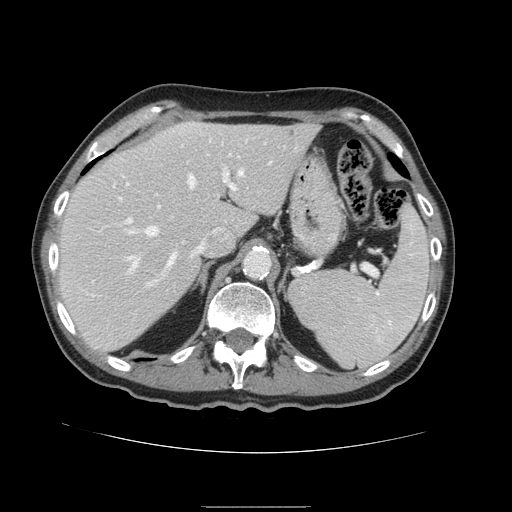
Contrast-enhanced abdominal CT, one axial slice; position 108 of 168 along the scan axis; soft-tissue window (W 400 / L 40 HU); 512 × 512 image matrix. Male patient, age 74 years. From the clinical record (not read from this slice): diagnosis: colorectal cancer liver metastases, imaged before liver resection; multiple liver metastases: no; largest metastasis: 14.5 cm; disease in both lobes: yes.
Outlined on this slice (expert manual segmentation):
- hepatic veins: bounding box <130,170,243,269> (left, top, right, bottom; pixels)
- liver: <58,122,320,352>
- planned liver remnant (the part of the liver to remain after resection): <59,122,320,352>
- portal vein (with intrahepatic branches): <93,184,236,286>